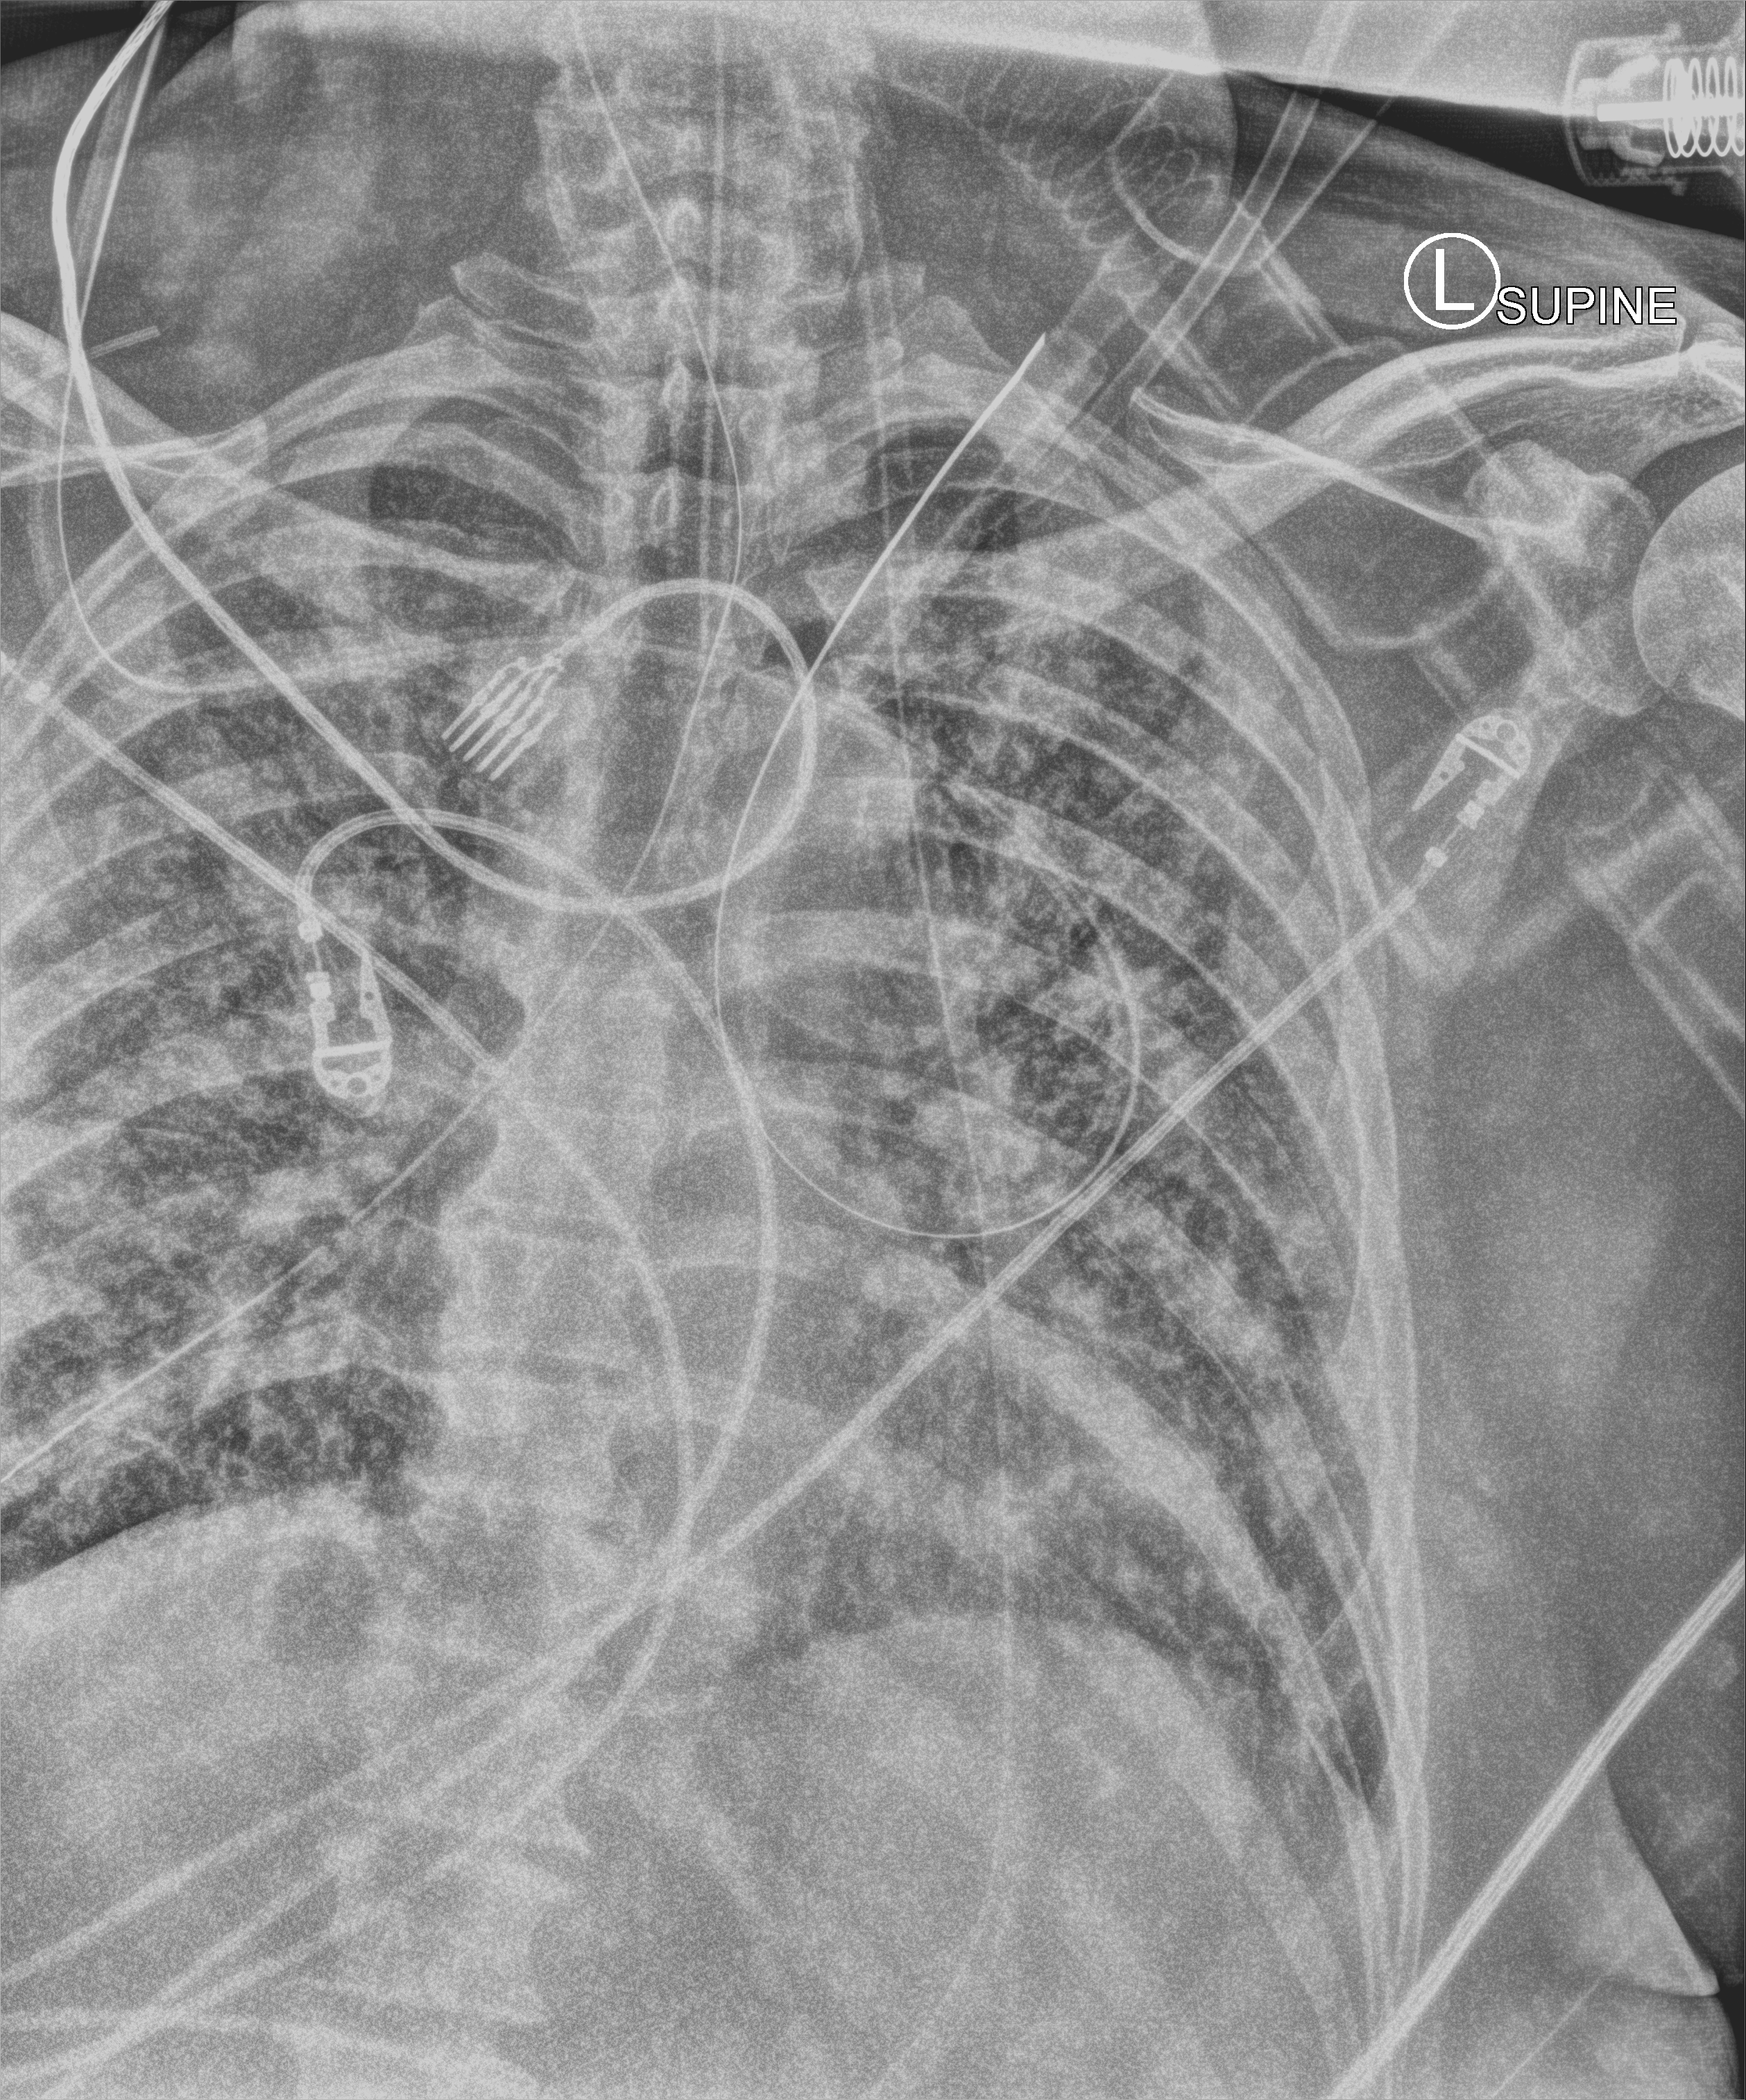
Bedside chest radiograph (computed radiography), anteroposterior (AP) projection. Patient hospitalised with COVID-19; male, aged 60–74 years.
Hospital-stay facts (about this admission, not read from this image; timing relative to this image not recorded): admitted to intensive care during this hospital stay: yes; length of hospital stay: 40 days; smoking status (admission record): former.